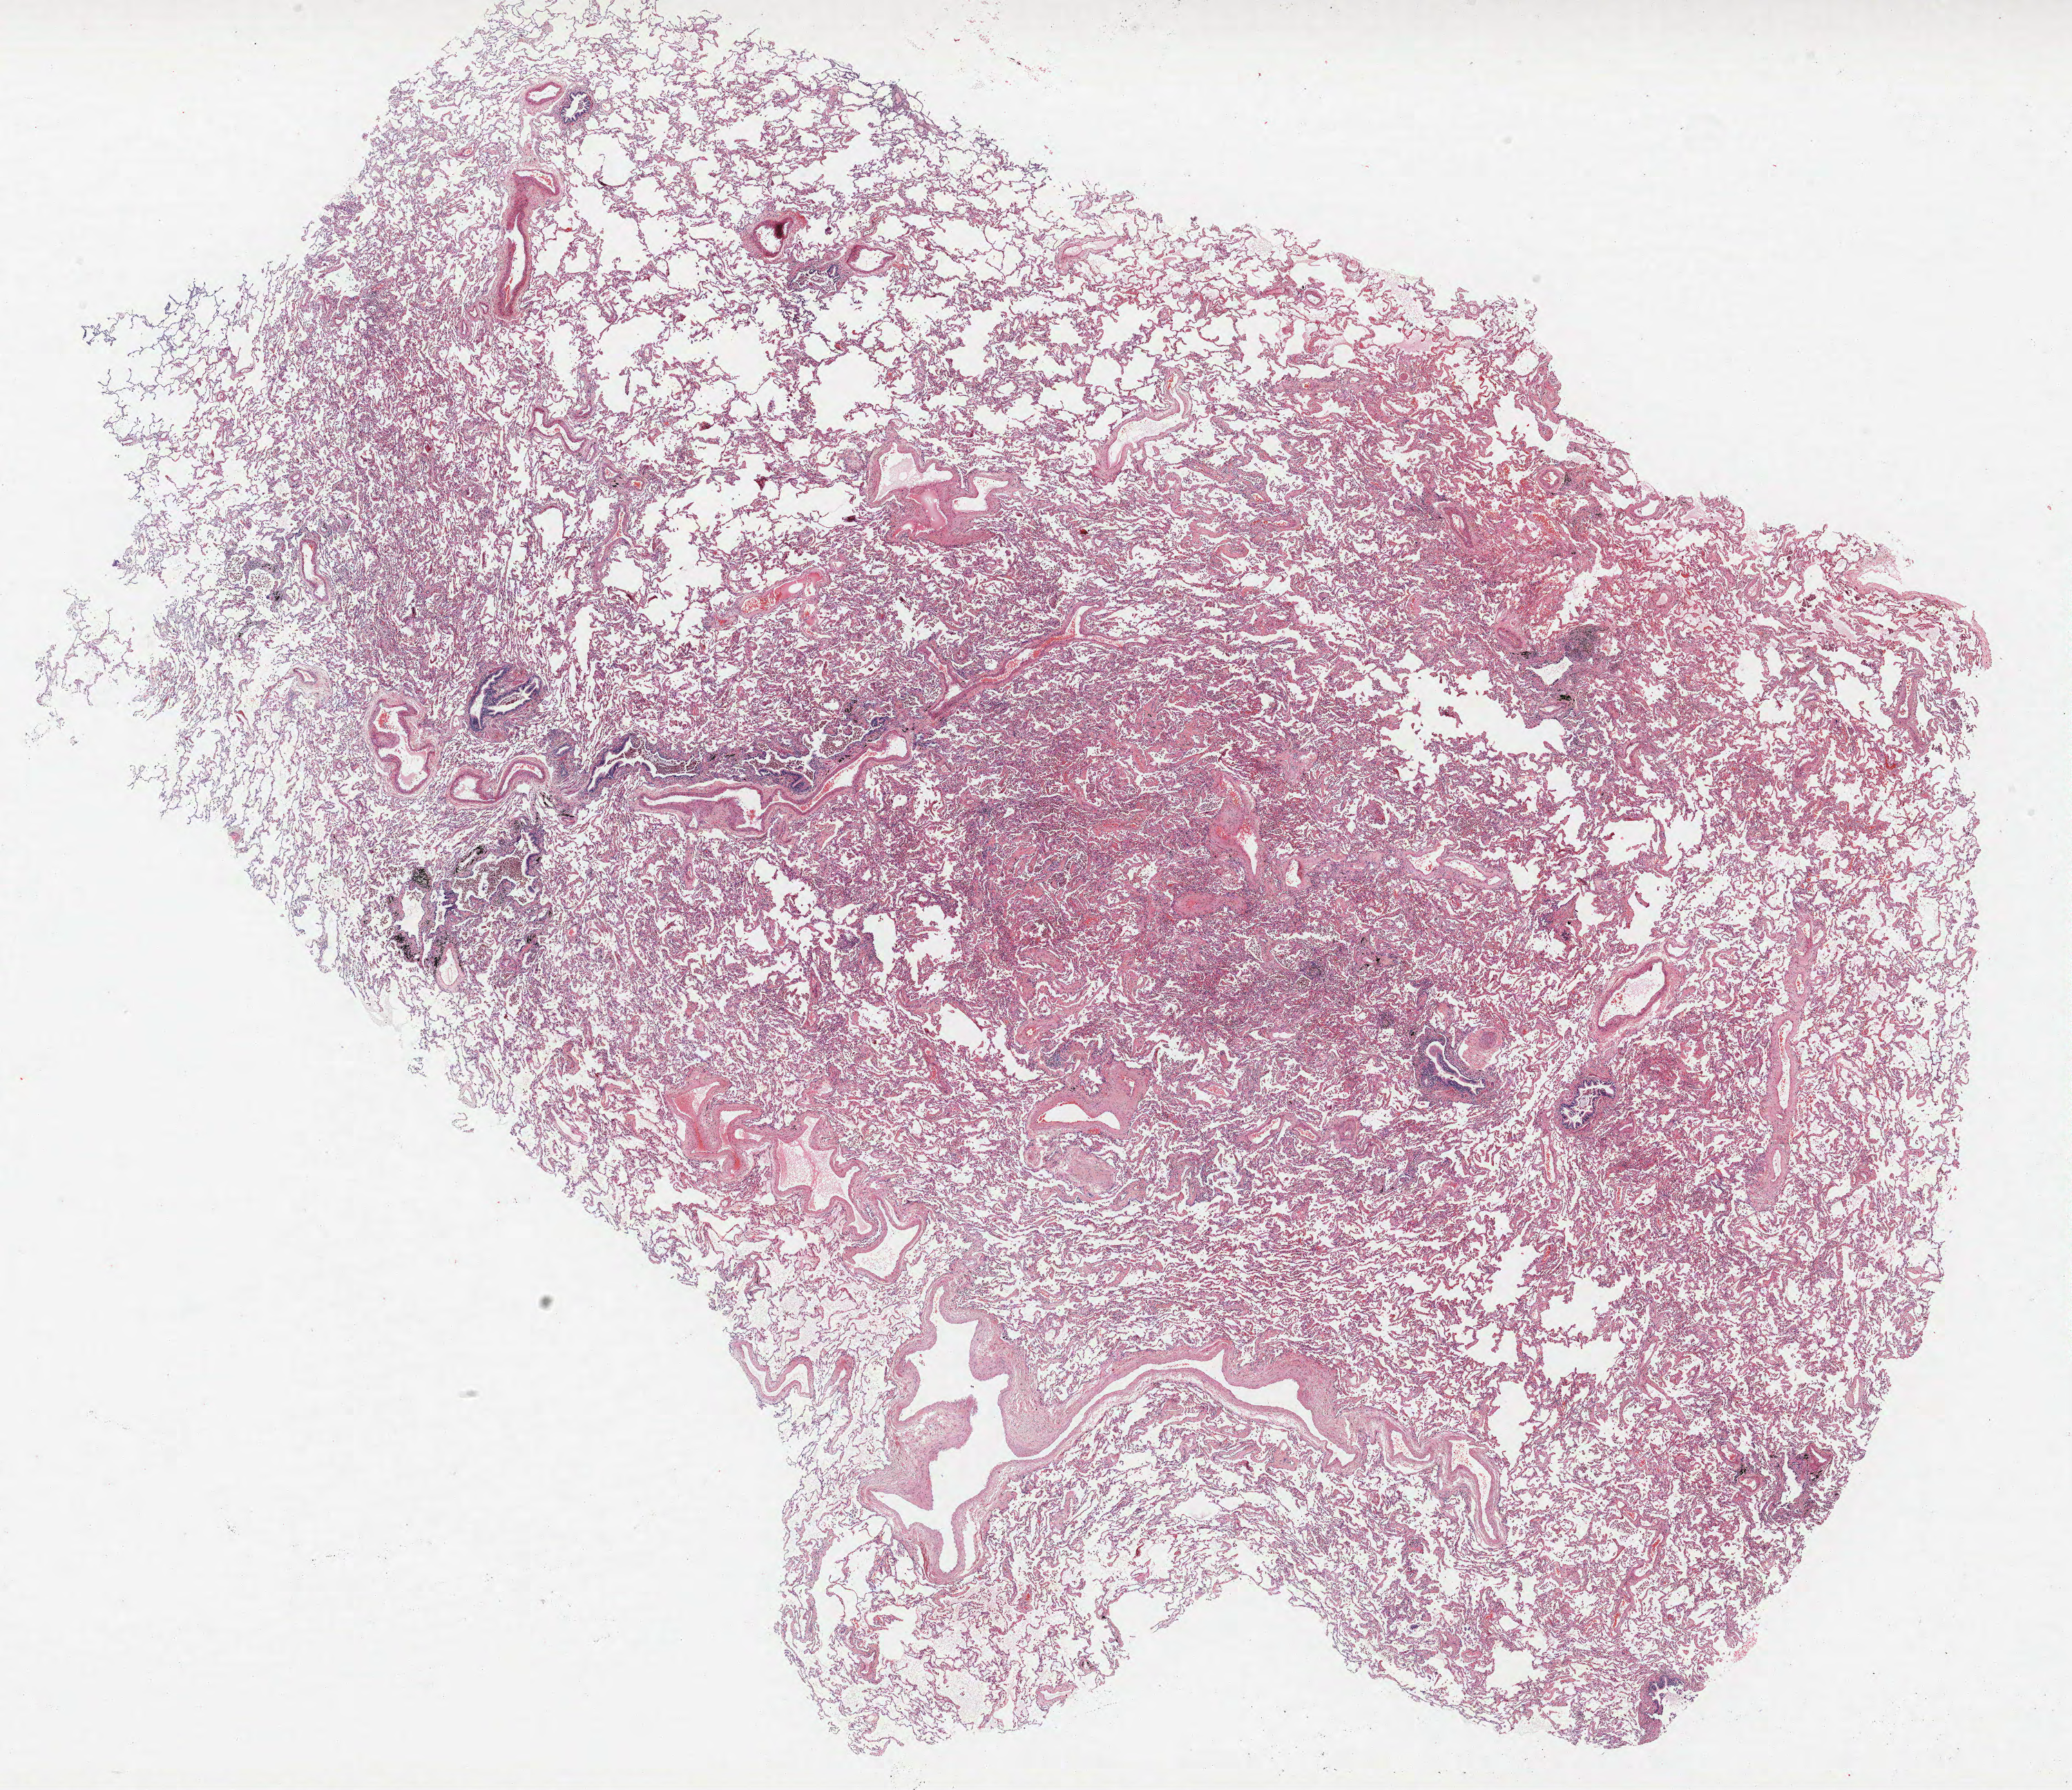
Whole-slide histology image, H&E-stained, a low-resolution overview of the entire scanned area, about 24.0 x 20.7 mm (acquisition: 40x scan); FFPE section; lung. Female patient, aged 59 at enrolment. Current smoker at enrolment. Grade: poorly differentiated (G3).
* participant's lung-cancer diagnosis: Adenocarcinoma, NOS
* stage (AJCC 6th edition): IA
* primary tumour location (clinical record): left lower lobe
* tumour size (pathology): 22 mm